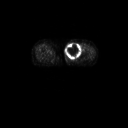
FDG PET of an extremity soft-tissue mass (from a PET/CT study), one axial slice. Slice 31 of 91 in the series (ordered by position). 3.27 mm slice thickness. 128 × 128 image matrix, field of view 700 × 700 mm. Female patient, age 74 years. Case-level facts recorded for this patient, not image findings: histological type: pleomorphic leiomyosarcoma; grade: high; site of the primary tumour: left thigh.
Structures marked on this image (expert contour drawn on MRI and transferred to this co-registered scan by the dataset authors):
- gross tumour volume including surrounding oedema: bounding box <65,42,82,59> (left, top, right, bottom; pixels)
- gross tumour volume (mass): <65,42,82,59>